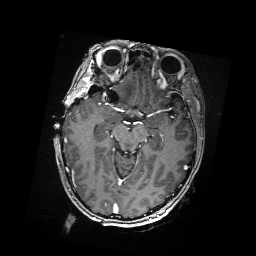
Brain MRI from a brain-tumour surgery series, one axial slice. Slice 106 of 176 in the series (ordered by position). T1-weighted post-contrast. 1 mm slice thickness. 256 × 256 image matrix, field of view 256 × 256 mm. Case-level facts recorded for this patient, not image findings: histopathology: Metastatic Carcinoma from Breast primary; tumour location: Right Frontal.
Annotated regions visible in this slice (expert manual segmentation):
- residual tumour: box from (x=109, y=86) to (x=116, y=97) px